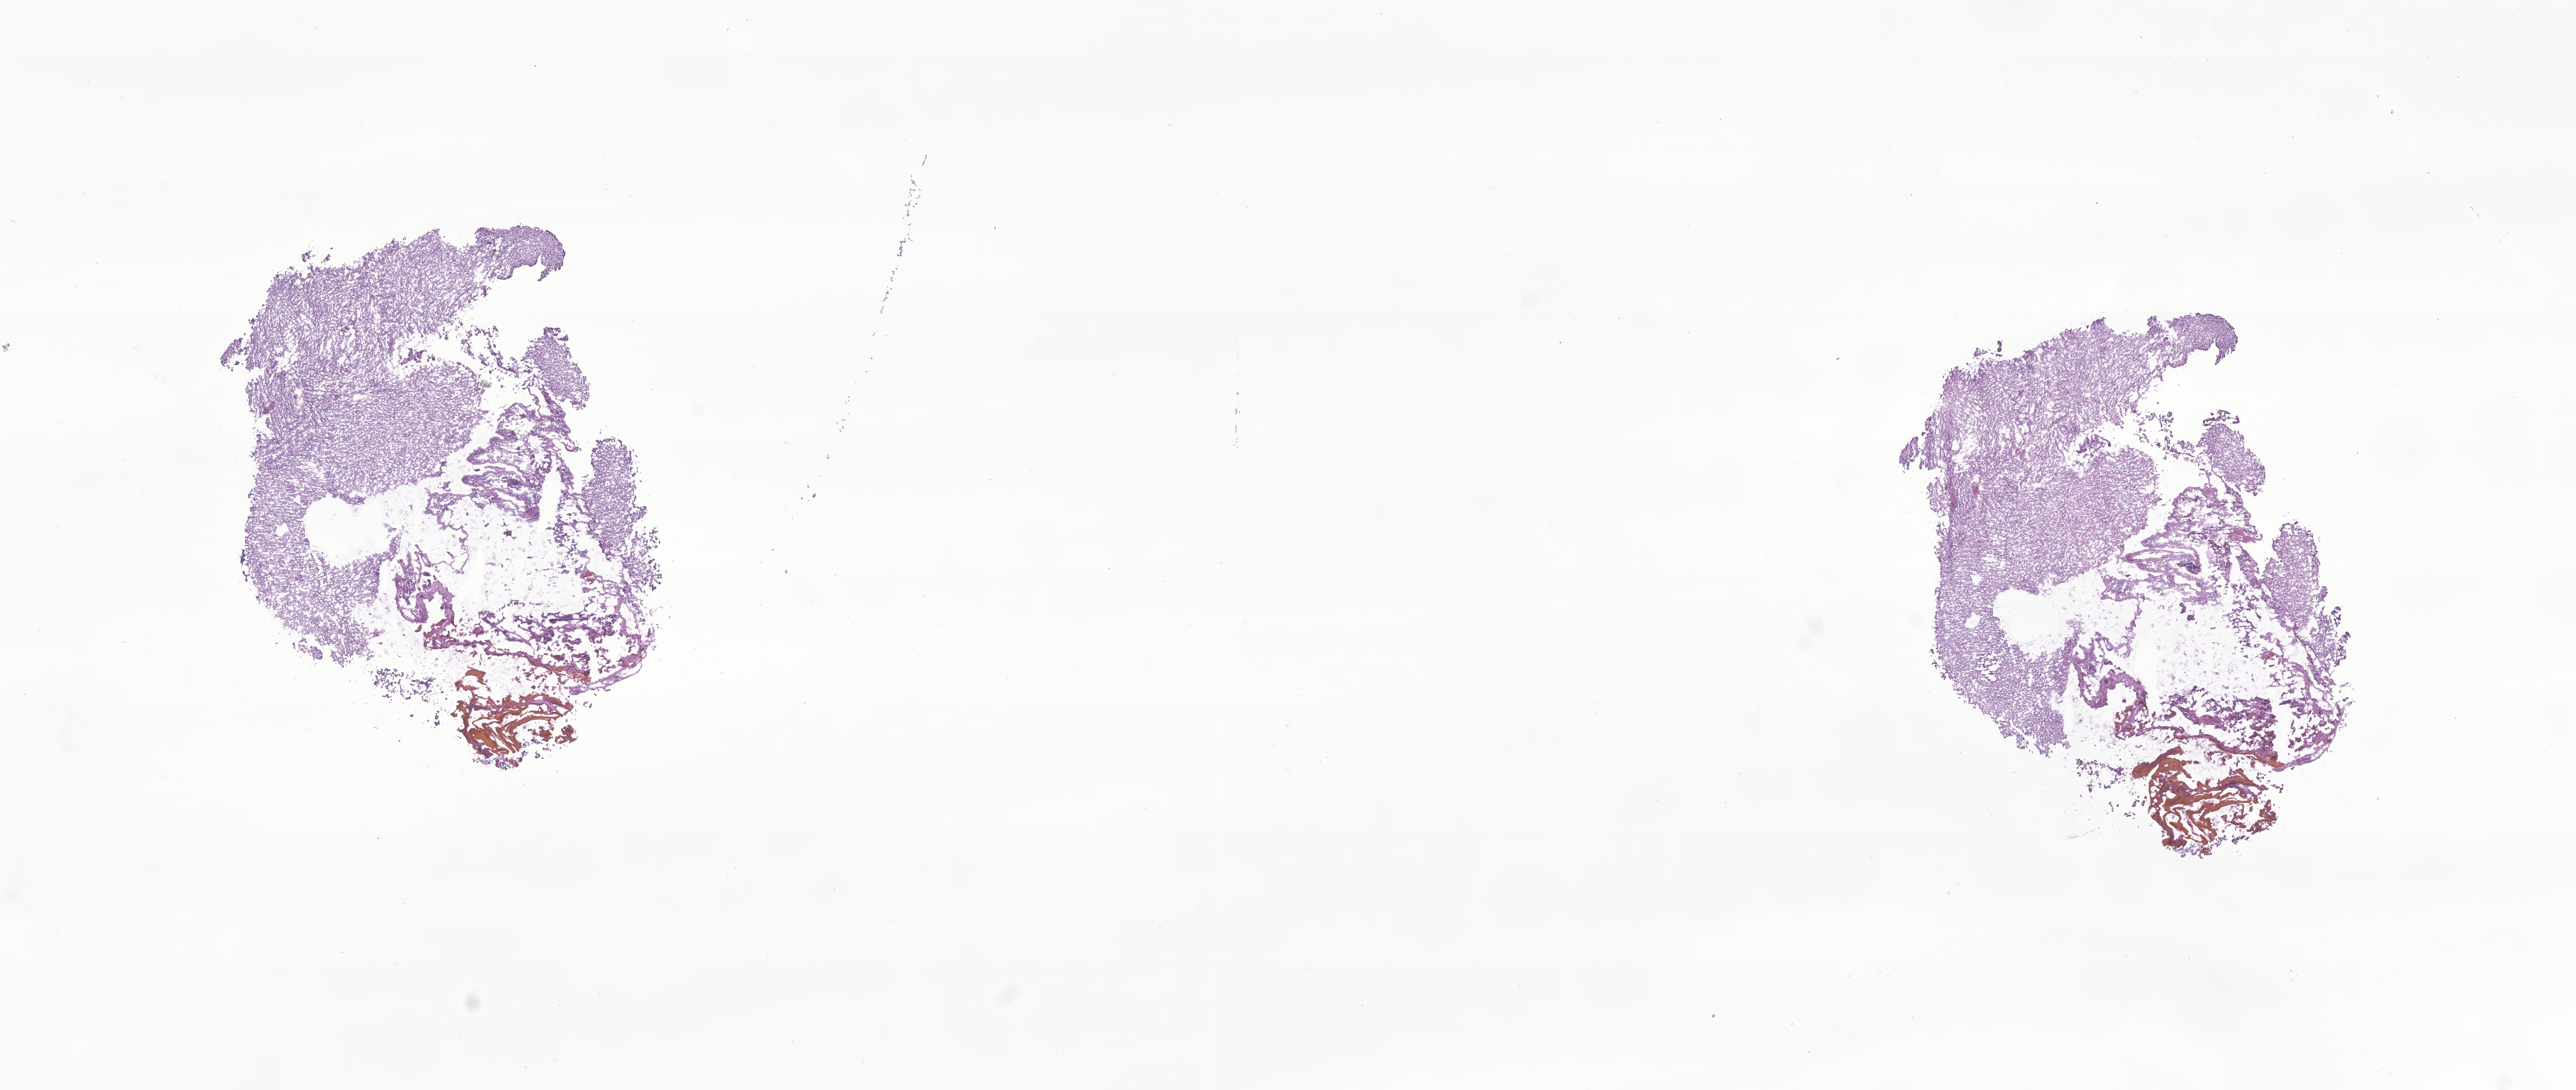
Haematoxylin and eosin whole-slide image of tumor tissue from the parietal lobe, low-resolution overview of the scanned area, about 21.2 x 9.0 mm, cryosection (OCT / tissue freezing medium). Patient female; age 78 months.
Diagnosis (ICD-O-3 morphology term): Ependymoma, NOS.